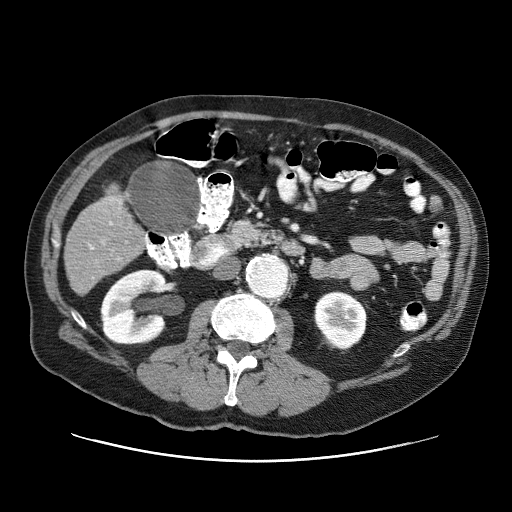
Contrast-enhanced abdominal CT (liver protocol), one axial slice; slice 15 of 87 in the series (ordered by position); reconstruction kernel STANDARD; 120 kVp; one of 3 acquisitions stored at this slice position; soft-tissue window (W 400 / L 40 HU); 2.5 mm slice thickness; 512 × 512 image matrix, field of view 400 × 400 mm. Case-level facts recorded for this patient, not image findings: diagnosis: hepatocellular carcinoma (patient treated with transarterial chemoembolisation; whether this scan precedes or follows treatment is not stated here); TNM stage (as recorded): Stage-IIIA; Child-Pugh class: A; tumour differentiation: well differentiated; tumour nodularity: multinodular.
Outlined on this slice (semi-automatic segmentation, software-assisted and operator-edited):
- liver parenchyma outside the tumour (the mass and vessels are separate outlines, so this box may not span the whole liver): bounding box <64,184,142,294> (left, top, right, bottom; pixels)
- liver vessels: <89,198,121,250>